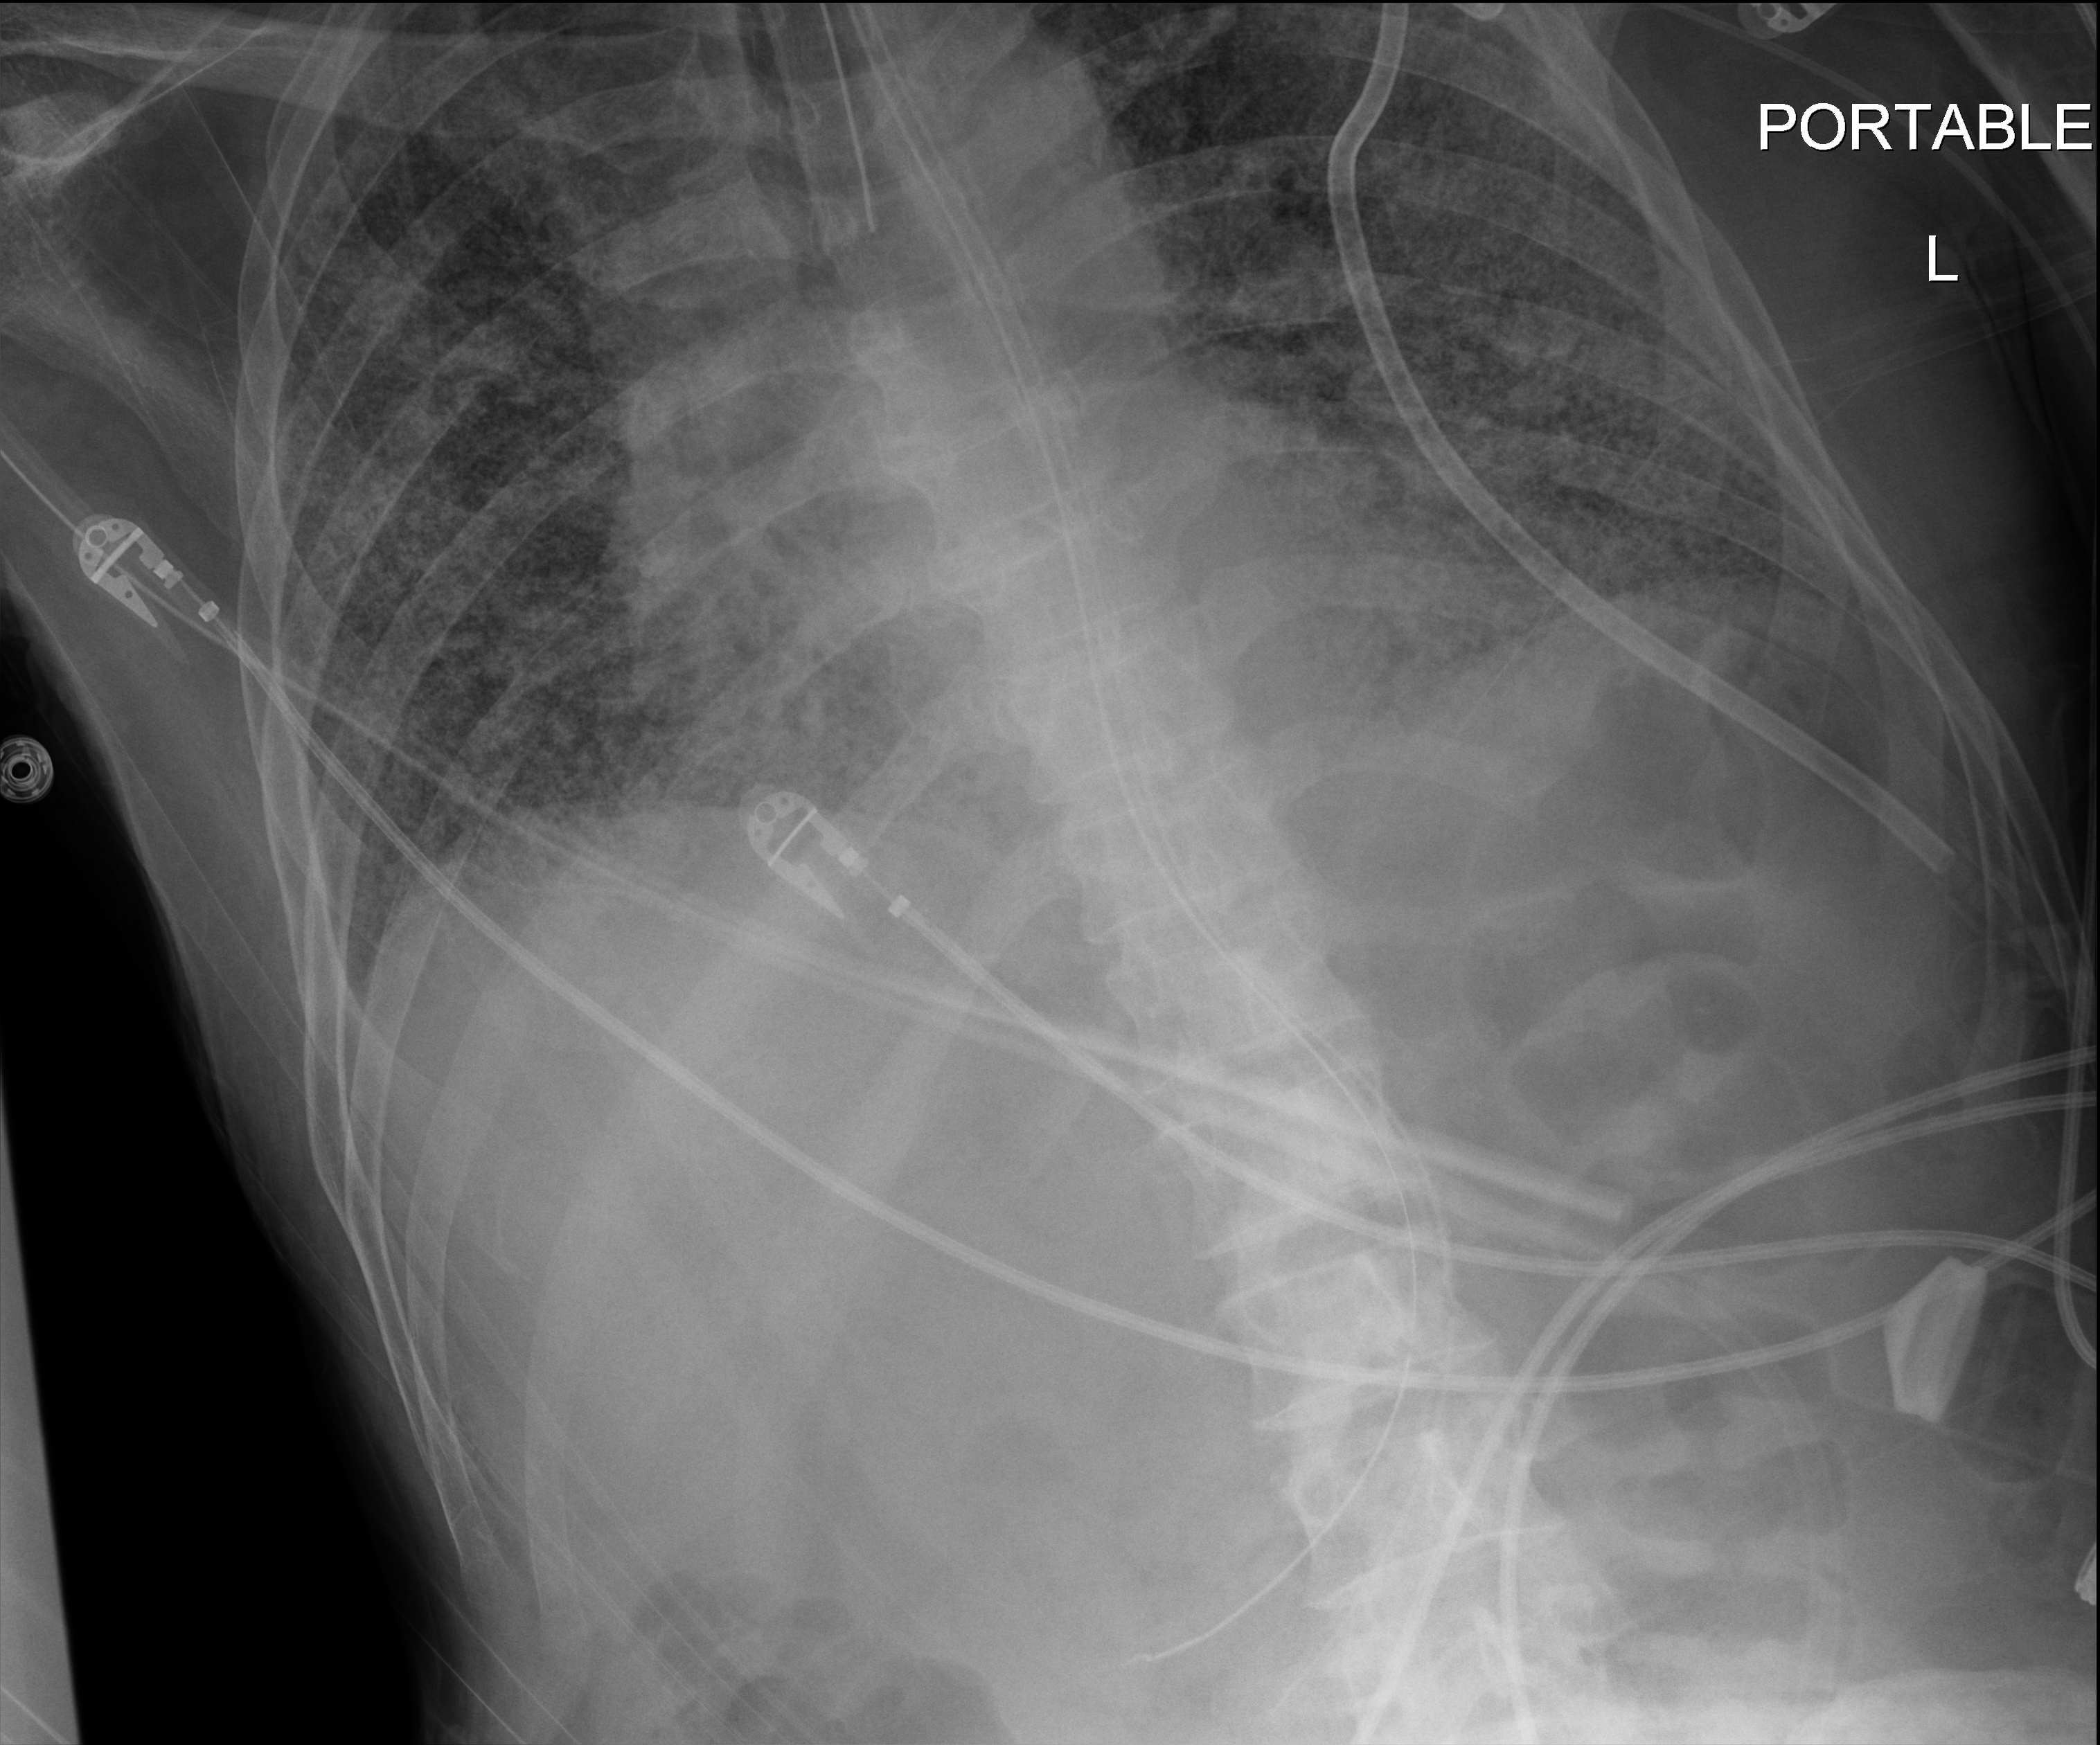
Chest X-ray, anteroposterior (AP) projection. Male patient hospitalised with COVID-19, age 60–74 years.
Admission-level facts for this patient (not findings on this image; timing relative to this image not recorded):
- length of hospital stay: 54 days